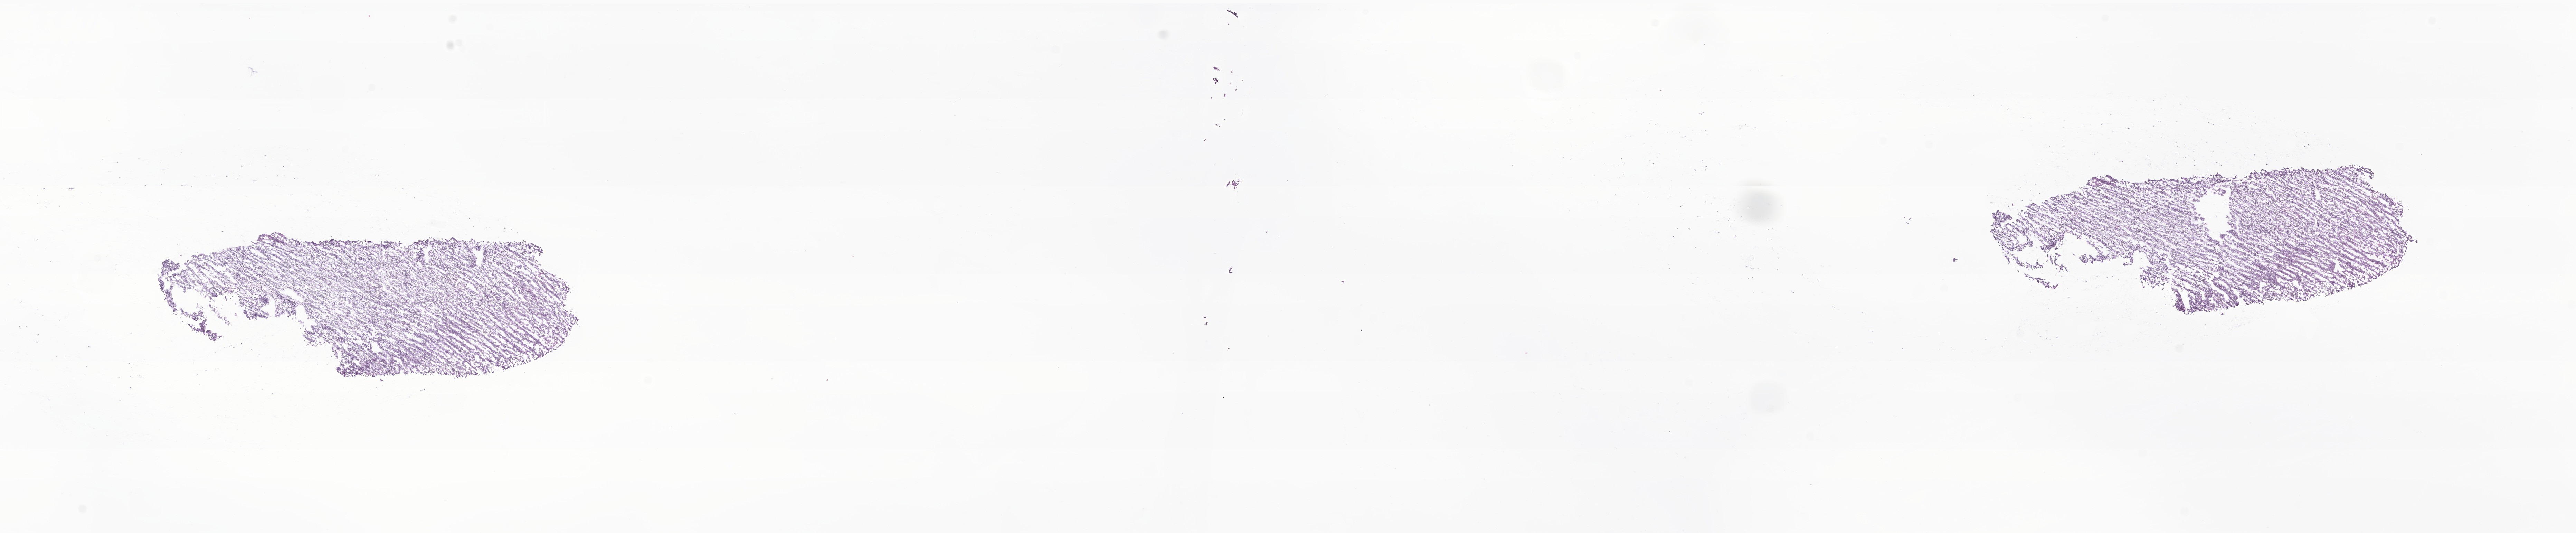
Haematoxylin and eosin whole-slide image of tumor tissue from the brain, shown as a low-resolution overview of the whole scanned area (about 31.4 x 6.5 mm). Frozen section. Female patient, age 989 days (about 2.7 years).
- recorded diagnosis: Medulloblastoma, NOS